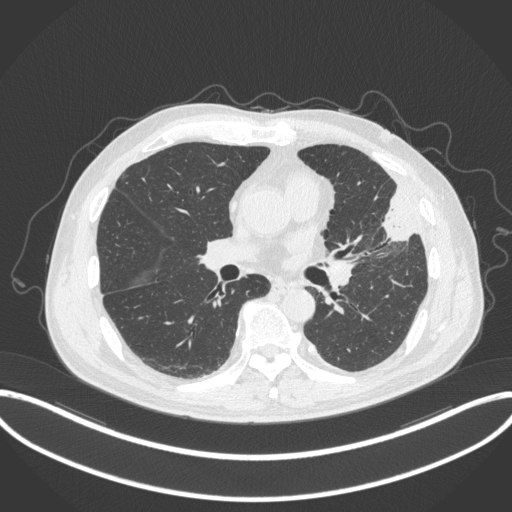
Chest CT, one axial slice. Position 175 of 382 along the scan axis. Lung window (W 1500 / L -600 HU). 512 × 512 image matrix, field of view 415 × 415 mm. Patient: male, 64 years. From the clinical record (not read from this slice): clinical TNM (as recorded): T4 N1 M0.
Annotated regions visible in this slice (rectangle marked by the reading radiologist):
- lung tumour (recorded histology: adenocarcinoma): bounding box <378,184,417,246> (left, top, right, bottom; pixels)